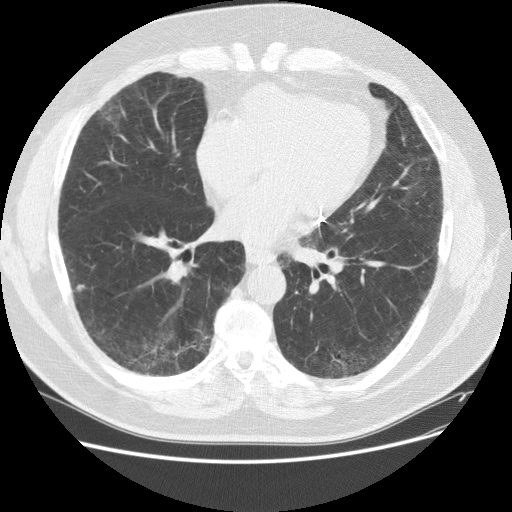
Chest CT (low-dose screening protocol), one axial image, baseline annual screen, lung window (W 1500 / L -600 HU), standard (soft-tissue) reconstruction kernel (STANDARD). Male participant, aged 59 years at enrolment. Current smoker at enrolment.
Expert reader's lesion annotation, bounding box [x1, y1, x2, y2] px = [85, 88, 131, 139]. The screening reader recorded 2 non-calcified nodules or masses ≥4 mm on this exam (right middle lobe, right lower lobe); which of them this box marks is not recorded. Official screen result: positive, change unspecified: nodule(s) >= 4 mm or enlarging nodule(s), mass(es), or other non-specific abnormalities suspicious for lung cancer. Lung cancer was diagnosed 338 days after this screen: adenocarcinoma, NOS, right upper lobe, right middle lobe, moderately differentiated (G2), stage IA (AJCC 6th edition), 13 mm at pathology.